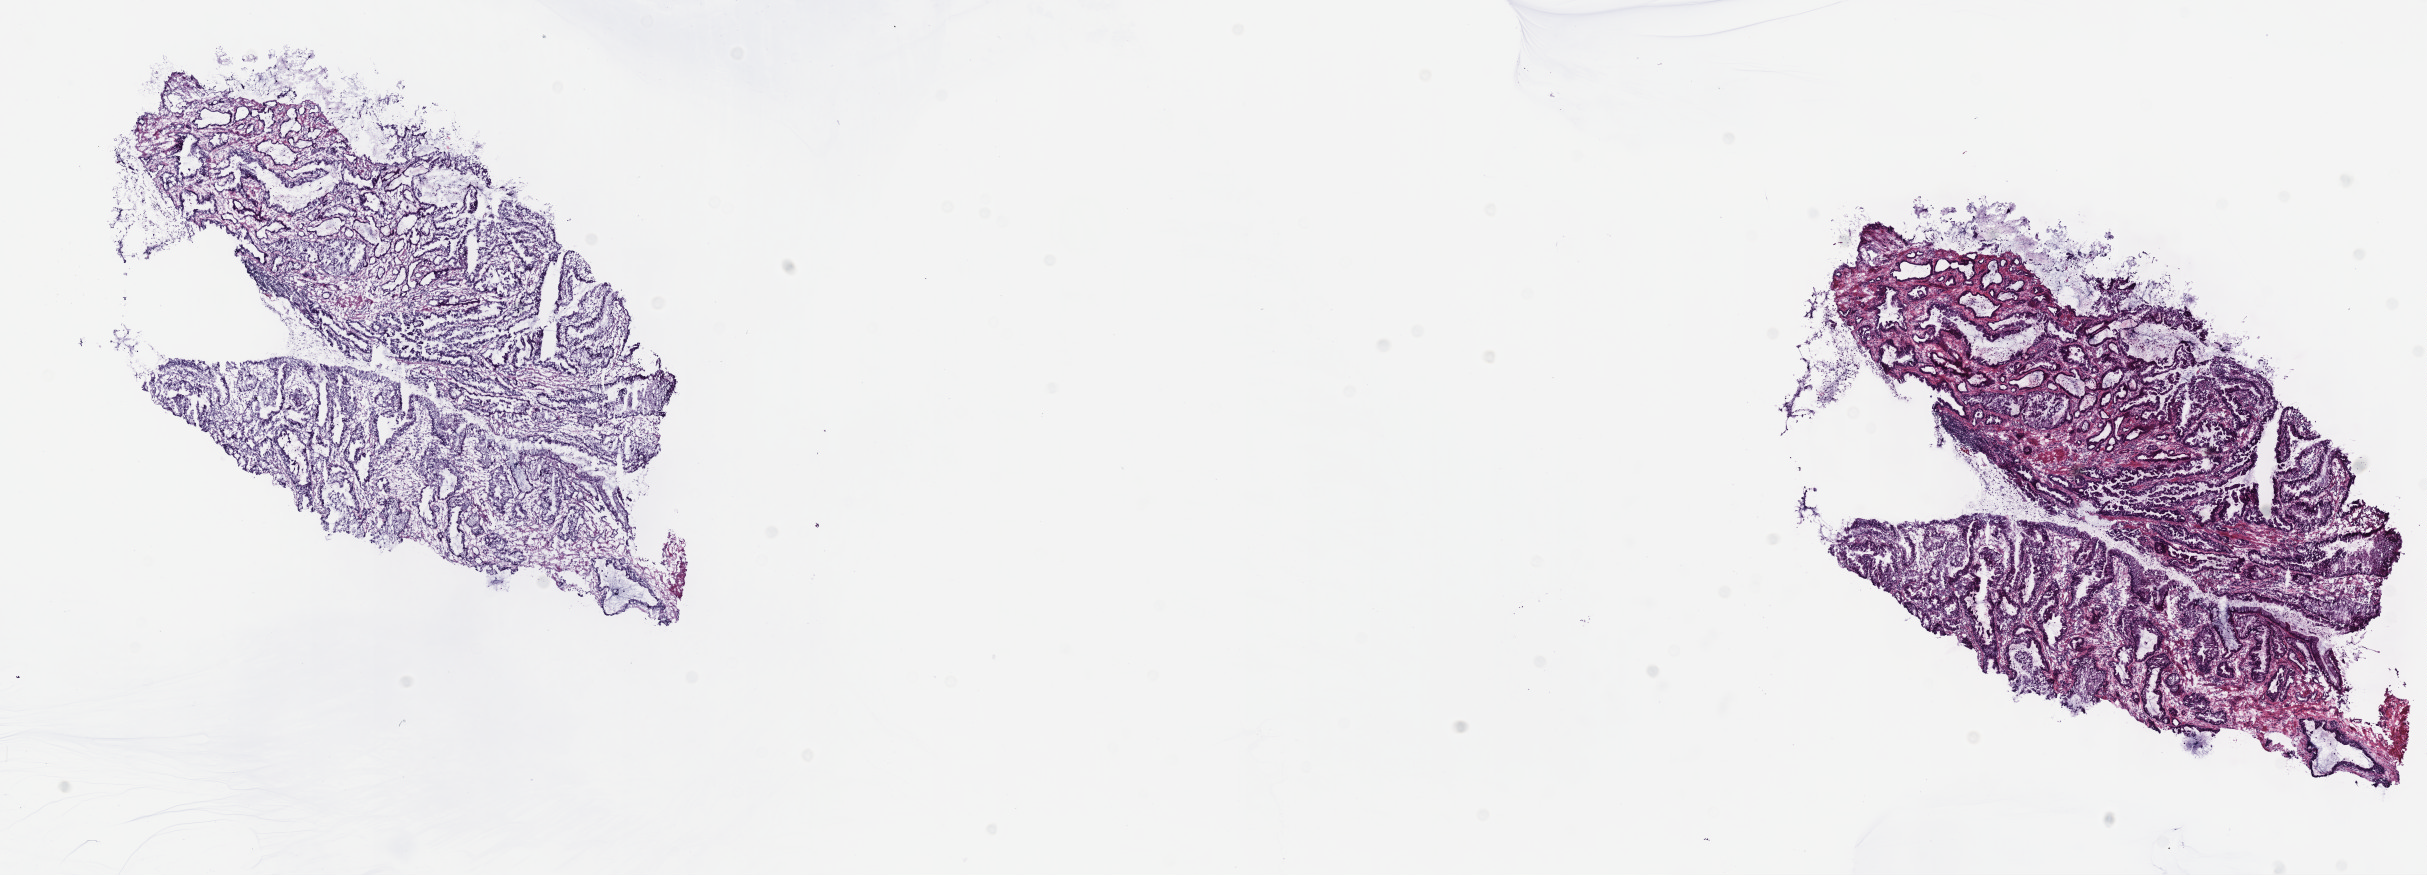
Digitized Hematoxylin and eosin (H&E) stained tissue section (whole slide) — a low-resolution overview of the entire scanned area, about 19.6 x 7.1 mm (from a 40x scan). Frozen section. Stomach, primary tumour sample. Patient: male, age at initial diagnosis 58 years. Histologic grade: G2 (moderately differentiated). Composition of this section per pathologist review: tumour cells 100%, tumour nuclei 60%, normal cells 0%, stromal cells 0%, necrosis 0%. Infiltration values recorded for this section: lymphocyte infiltration 5%, monocyte infiltration 0%, neutrophil infiltration 0%.
AJCC pathologic stage: IIIA (7th edition). Lymph nodes positive (case pathology): 4 of 10 examined. Diagnosis: Tubular adenocarcinoma (cardia, NOS).